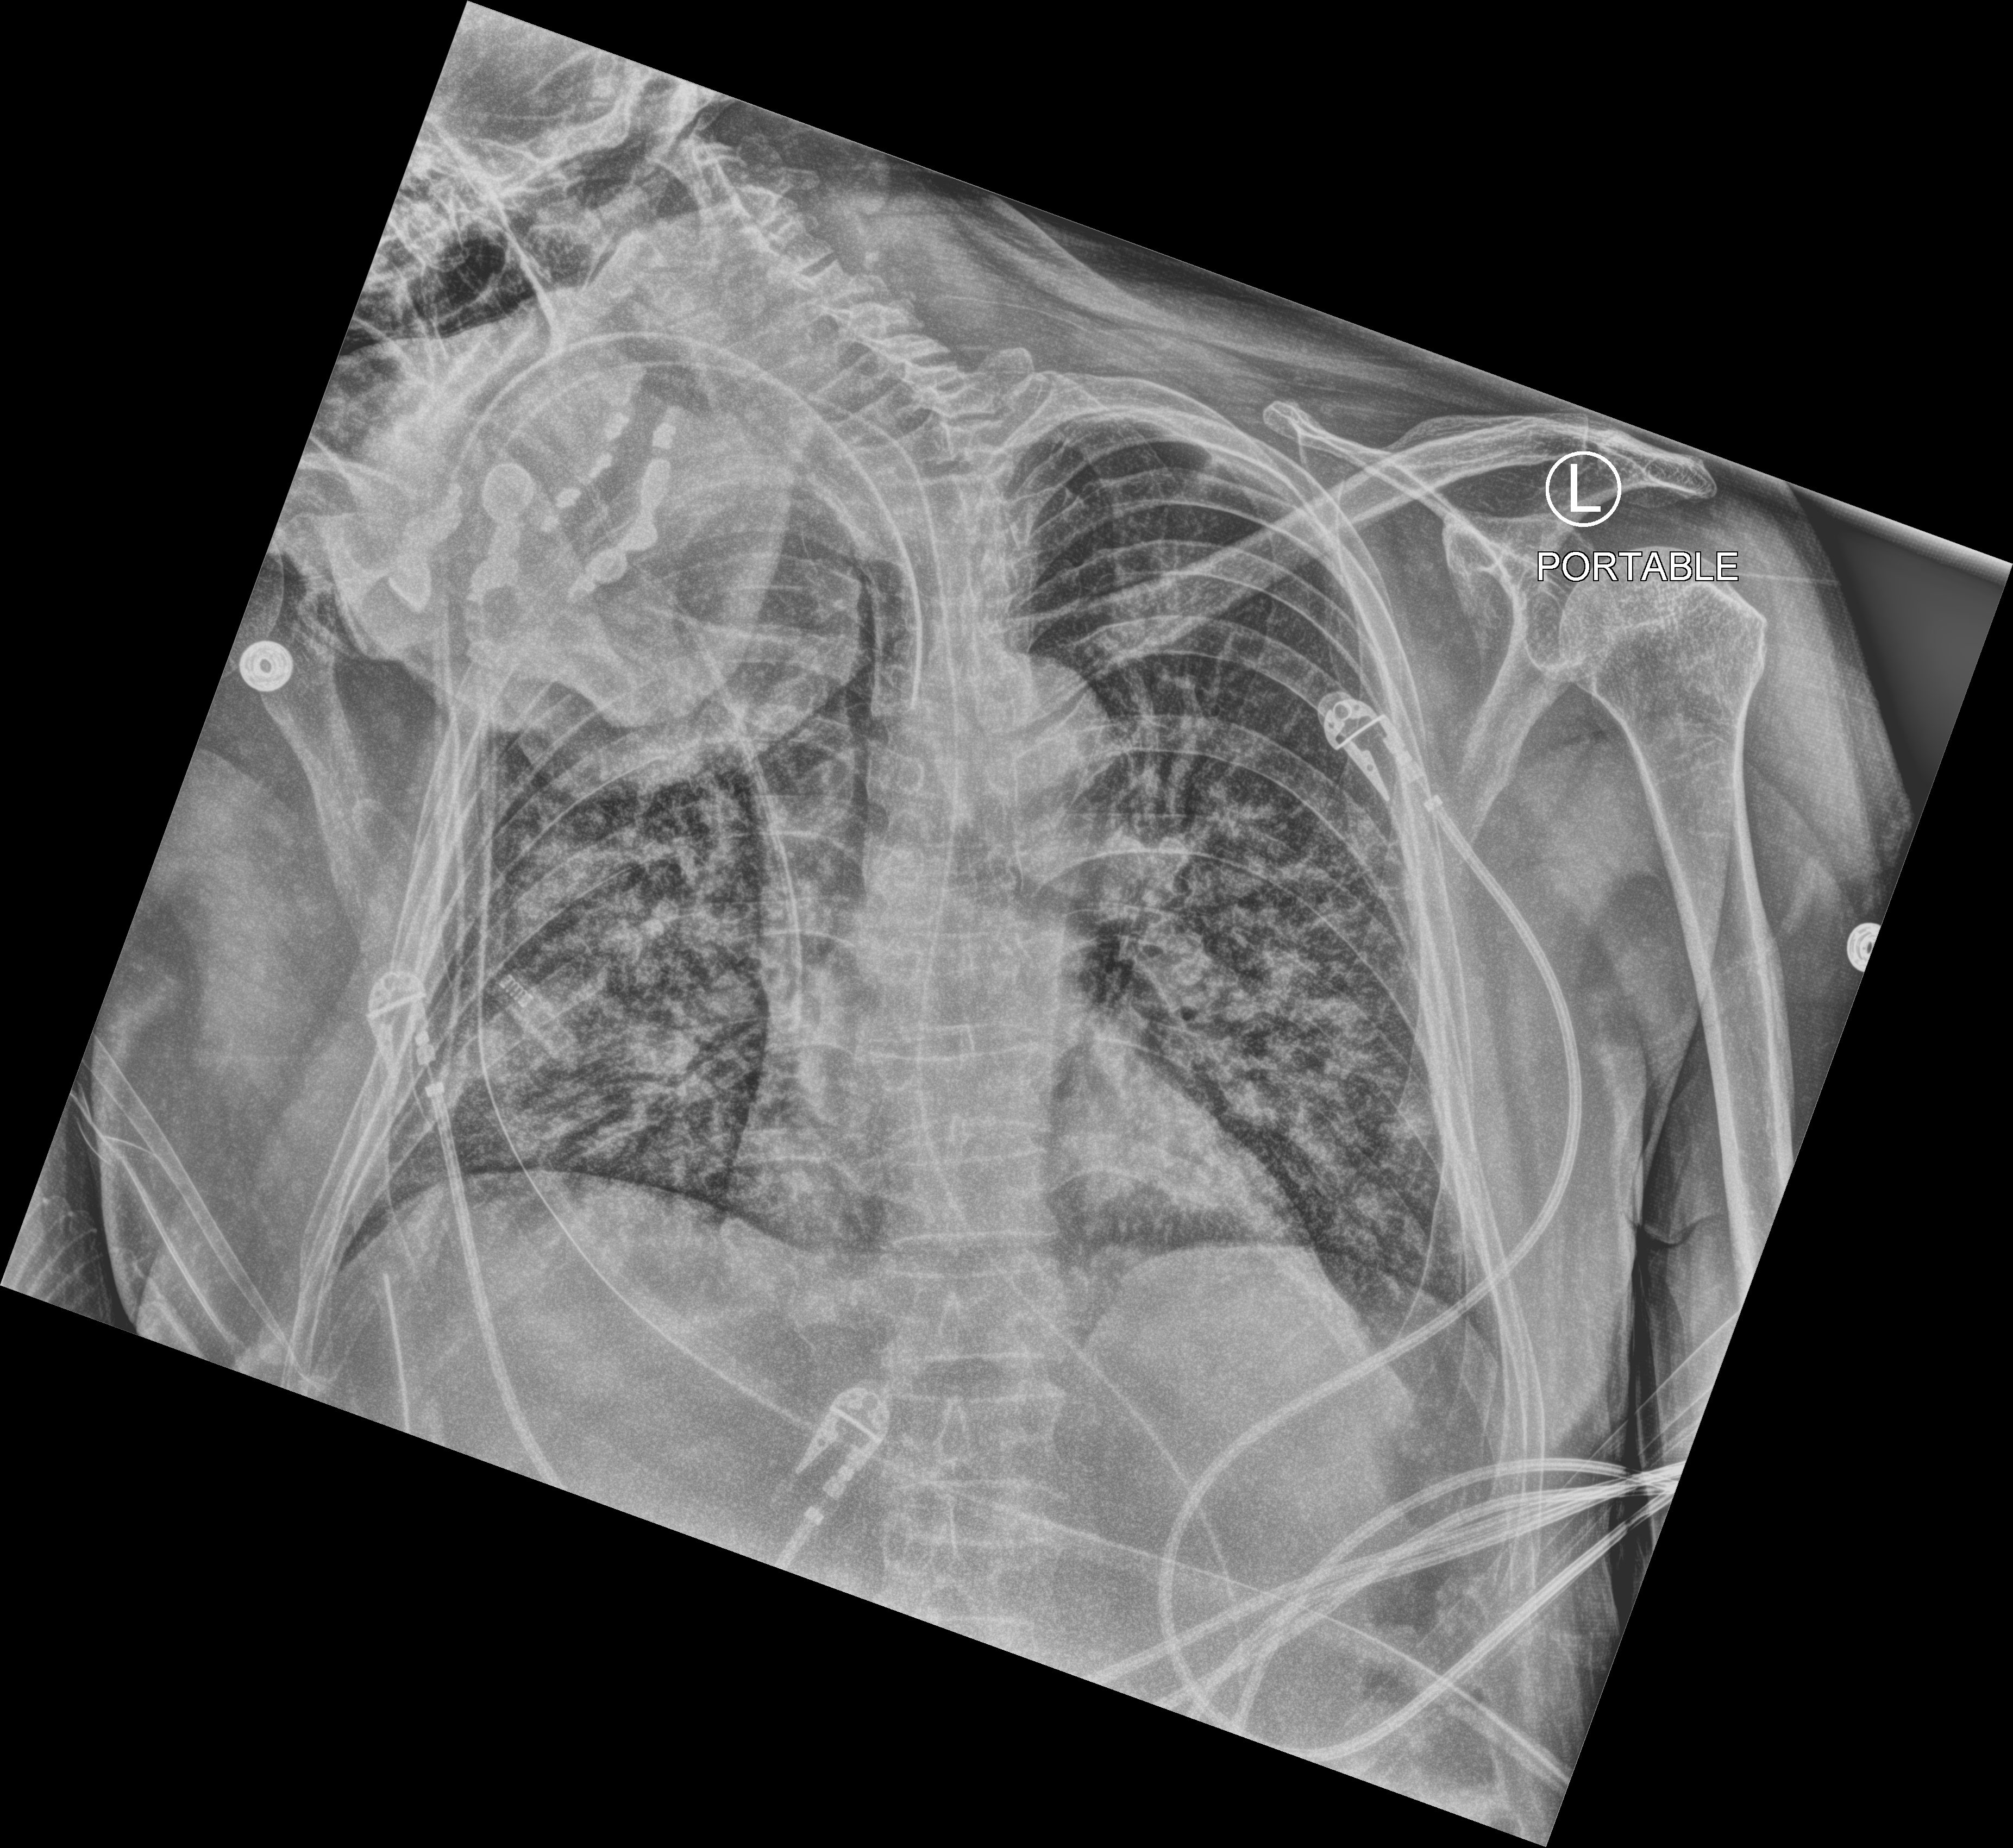
Portable chest radiograph, anteroposterior (AP) projection. Male patient hospitalised with COVID-19, age 60–74 years.
From the hospital-stay record, not from the radiograph (when in the stay this image was taken is not recorded):
- length of hospital stay: 19 days
- mechanically ventilated during this hospital stay: yes
- COPD (admission record): no